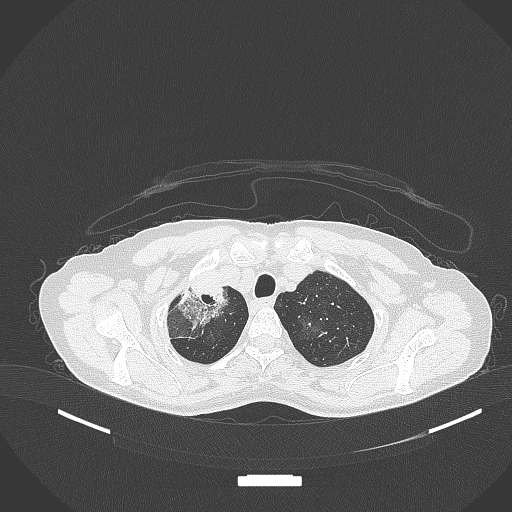
Chest CT, one axial slice. Position 281 of 284 along the scan axis. Reconstruction kernel B70f. 120 kVp. Lung window (W 1500 / L -600 HU). 1 mm slice thickness. 512 × 512 image matrix, field of view 400 × 400 mm. Patient: female, 59 years. From the clinical record (not read from this slice): clinical TNM (as recorded): T3 N0 M0.
Structures marked on this image (rectangle marked by the reading radiologist):
- lung tumour (recorded histology: adenocarcinoma): box from (x=173, y=279) to (x=229, y=330) px